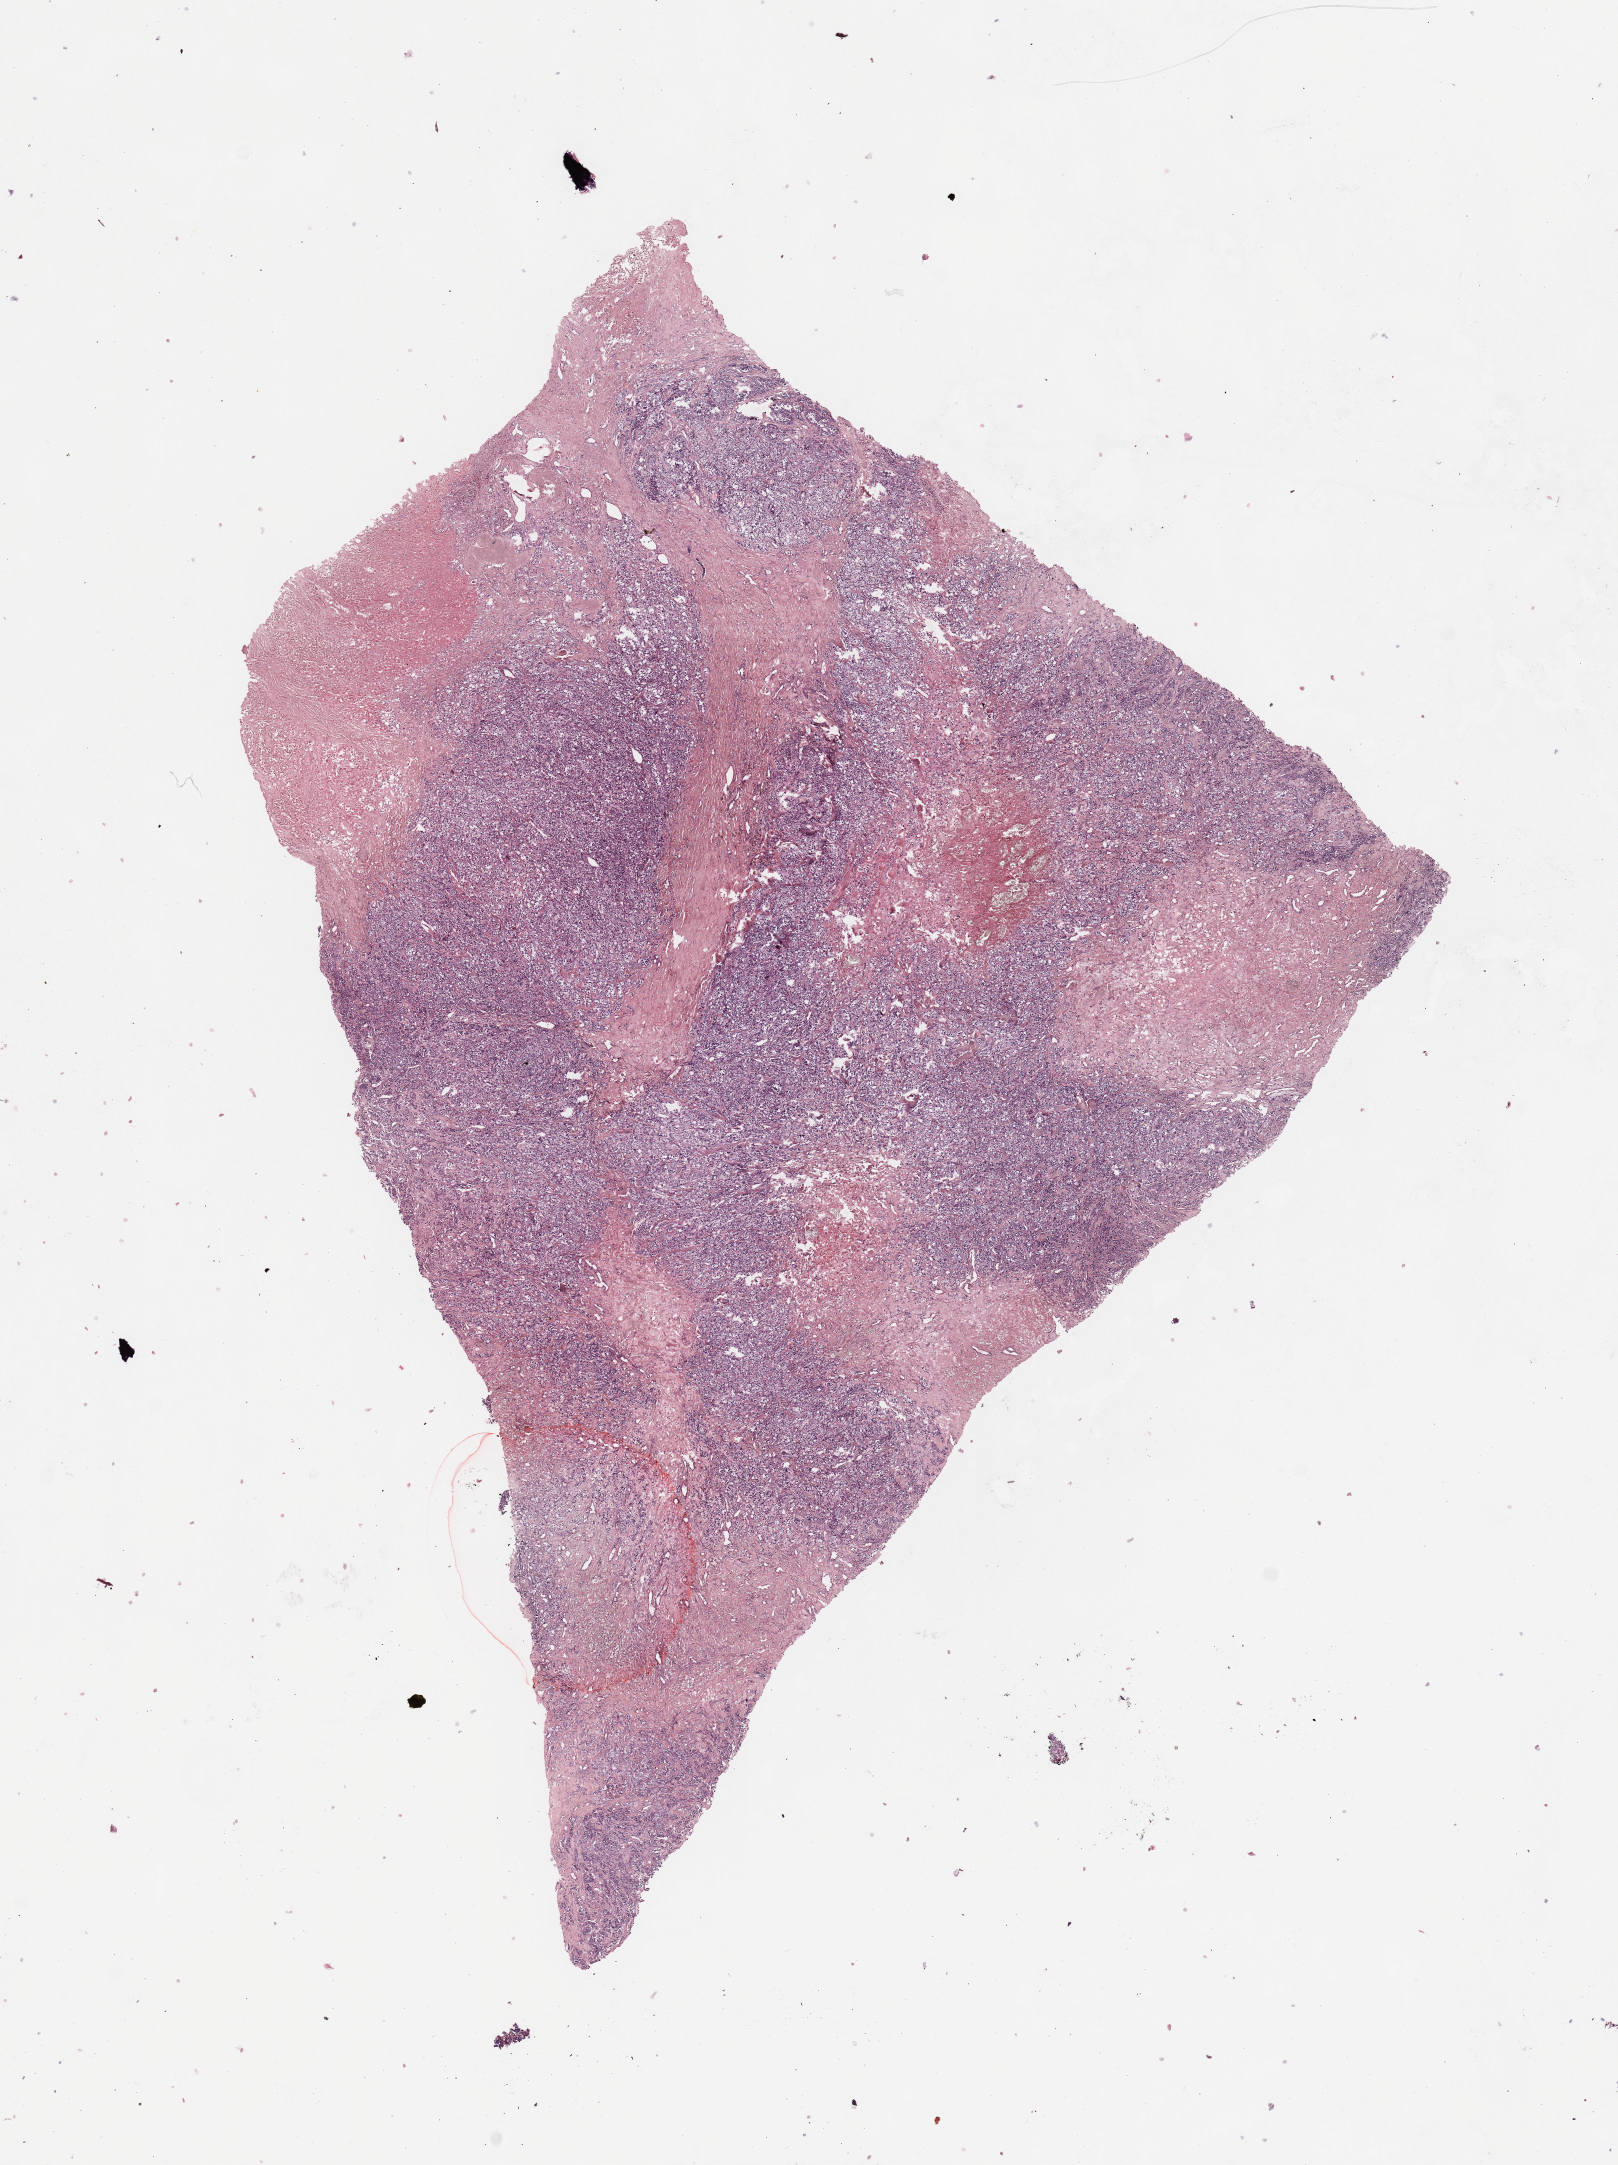
Whole-slide histology image, H&E — whole scanned area (about 12.8 x 17.1 mm, acquisition: 20x scan) shown as a low-resolution overview. Tumour tissue sample, sampled site: trunk. Patient: female, age 80 years. Pathologist review of this section (percent, as recorded): tumour nuclei 80%, necrosis 20%.
This section: metastatic tumour tissue. Patient diagnosis: Malignant melanoma, NOS.